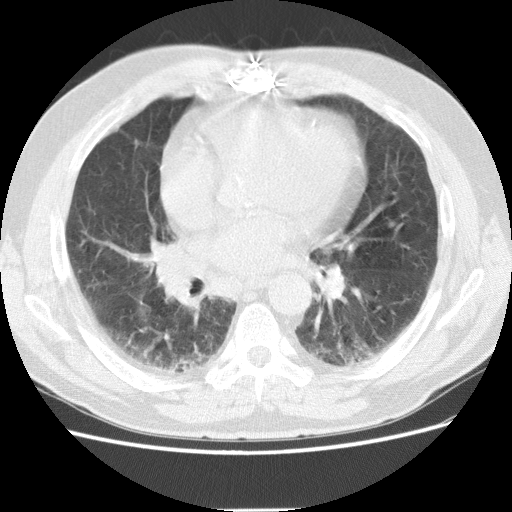
Chest CT (low-dose screening protocol), one axial image; first (baseline) screen; lung window (W 1500 / L -600 HU); 2.5 mm slice thickness; standard (soft-tissue) reconstruction kernel (STANDARD); slice 70 of 155 in the series. Male participant, aged 72 years at enrolment. Former smoker at enrolment.
Lesion marked by an expert reader, bounding box (x1, y1, x2, y2) in pixels: (146, 234, 195, 272). Screening reader's record for this exam: no non-calcified nodule ≥4 mm recorded. Official screen result: negative screen, minor abnormalities not suspicious for lung cancer. Participant outcome: lung cancer diagnosed 163 days after this screen — adenocarcinoma, NOS, right middle lobe, stage IIIB (AJCC 6th edition), 27 mm at pathology.